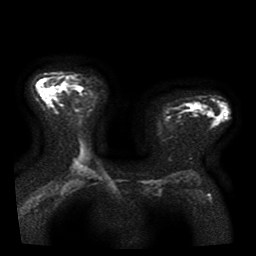
Breast MRI, one axial slice. Slice 26 of 41 in the series (ordered by position). Diffusion-weighted series; image 2 of 4 stored at this slice position (different b-values; order by instance number). 1.5 T. 256 × 256 image matrix. Female patient.
Structures marked on this image (outlined manually by an expert reader):
- tumour on diffusion-weighted imaging: bounding box <54,93,56,98> (left, top, right, bottom; pixels)